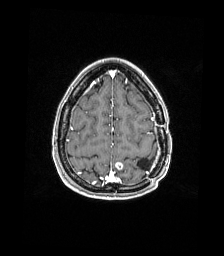
Brain MRI from a brain-tumour surgery series, one axial slice. Position 43 of 176 along the scan axis. T1-weighted post-contrast. 1 mm slice thickness. 224 × 256 image matrix. Case-level facts recorded for this patient, not image findings: histopathology: Atypical meningioma; WHO grade: 2.
Annotated regions visible in this slice (manually delineated by an expert):
- previous resection cavity: bounding box <137,158,150,170> (left, top, right, bottom; pixels)
- tumour: <115,162,124,170>